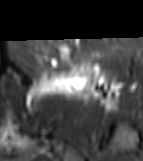
MRI of an extremity soft-tissue mass, one axial slice; slice 46 of 81 in the series (ordered by position); STIR; MR volume resampled by the dataset authors to the PET/CT grid (not the native acquisition matrix); 143 × 161 image matrix, field of view 140 × 157 mm. Female patient. Case-level facts recorded for this patient, not image findings: histological type: myxofibrosarcoma; grade: intermediate; site of the primary tumour: left thigh.
Annotated regions visible in this slice (expert contour drawn on MRI and transferred to this co-registered scan by the dataset authors):
- gross tumour volume including surrounding oedema: bounding box <24,62,125,107> (left, top, right, bottom; pixels)
- gross tumour volume (mass): <60,63,82,82>